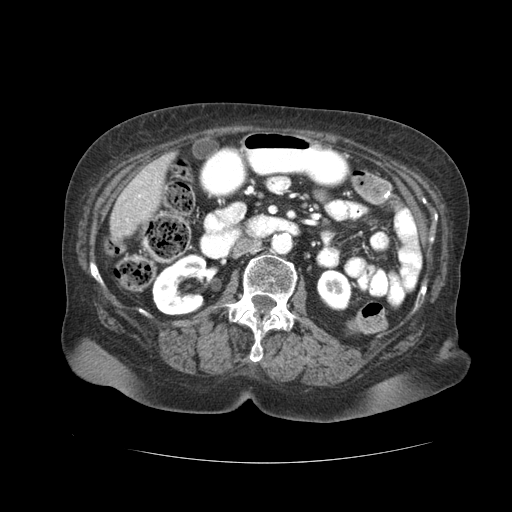
Contrast-enhanced abdominal CT (liver protocol), one axial slice; soft-tissue window (W 400 / L 40 HU); 2.5 mm slice thickness; 512 × 512 image matrix, field of view 380 × 380 mm. From the clinical record (not read from this slice): diagnosis: hepatocellular carcinoma (patient treated with transarterial chemoembolisation; whether this scan precedes or follows treatment is not stated here); TNM stage (as recorded): Stage-I; Child-Pugh class: A.
Structures marked on this image (semi-automatic segmentation, software-assisted and operator-edited):
- liver parenchyma outside the tumour (the mass and vessels are separate outlines, so this box may not span the whole liver): bounding box [x1, y1, x2, y2] px = [110, 152, 174, 242]
- liver vessels: [138, 195, 141, 197]